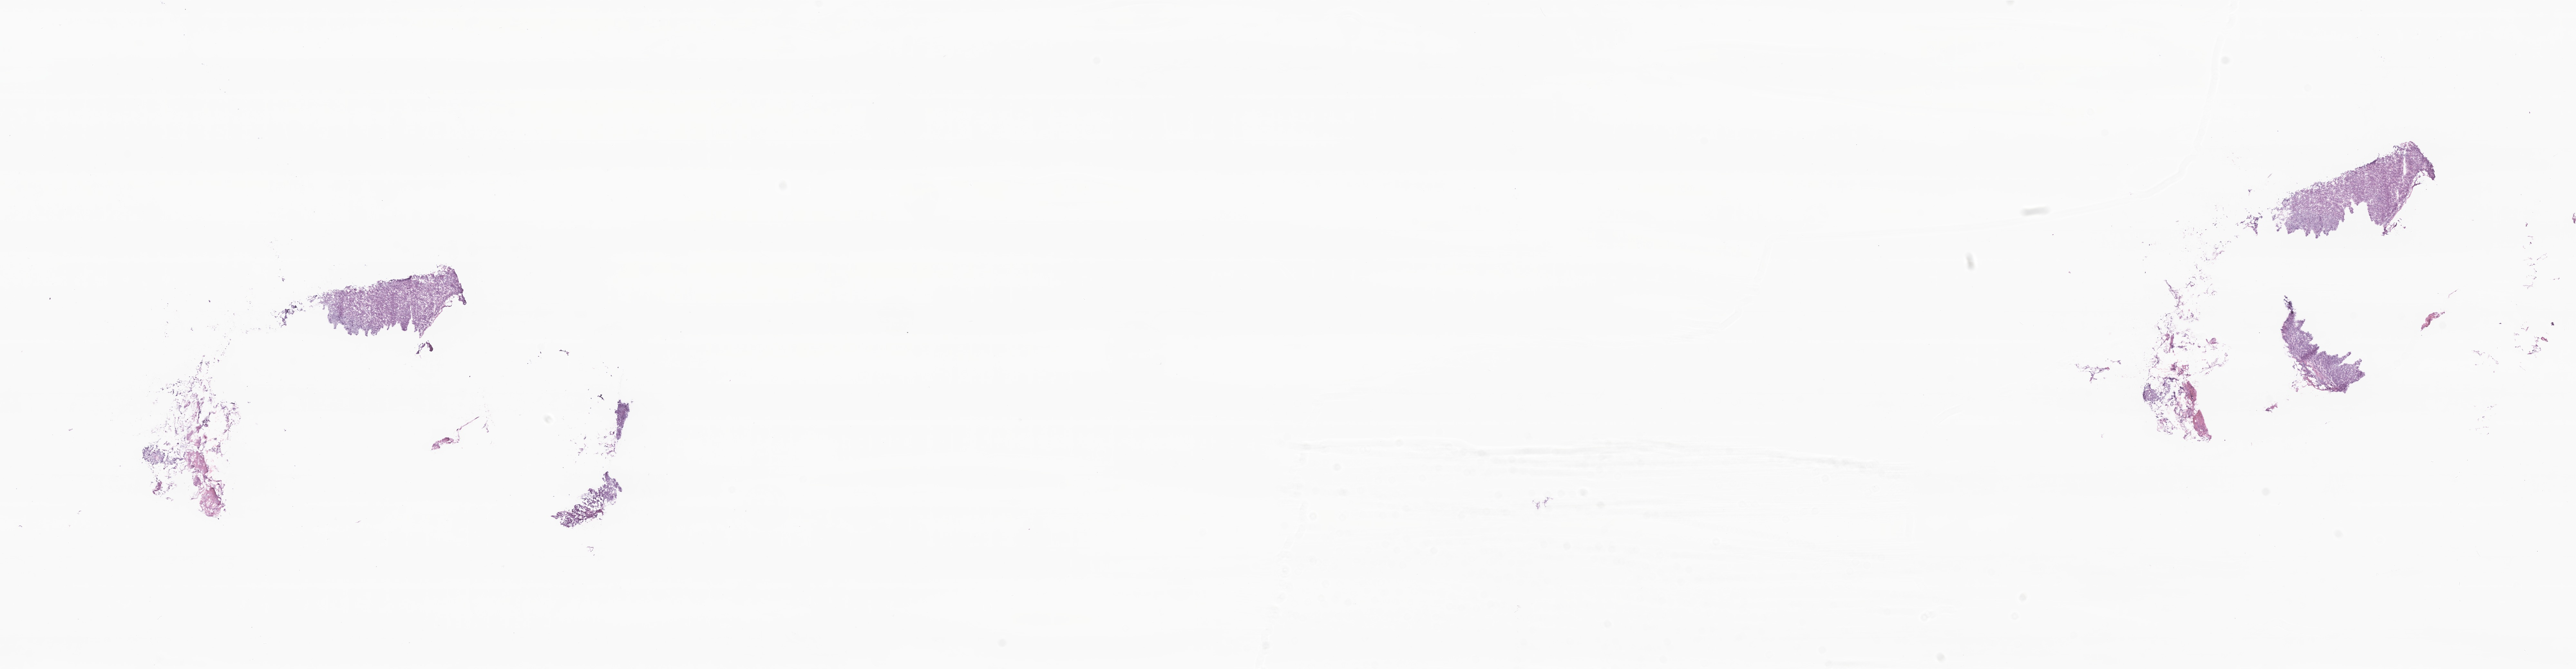
Haematoxylin and eosin whole-slide image, whole scanned area (about 33.7 x 8.8 mm) shown as a low-resolution overview. Frozen section (tissue freezing medium). Metastatic tumor tissue. Patient sex: female. Slide review estimates, as recorded: tumor cells 92%, tumor nuclei 95%, stromal cells 3%, necrosis 0%, normal cells 5%. Infiltration values recorded for this section: lymphocyte infiltration 5%, monocyte infiltration 0%, neutrophil infiltration 0%.
Patient diagnosis (primary): Lobular carcinoma, NOS.